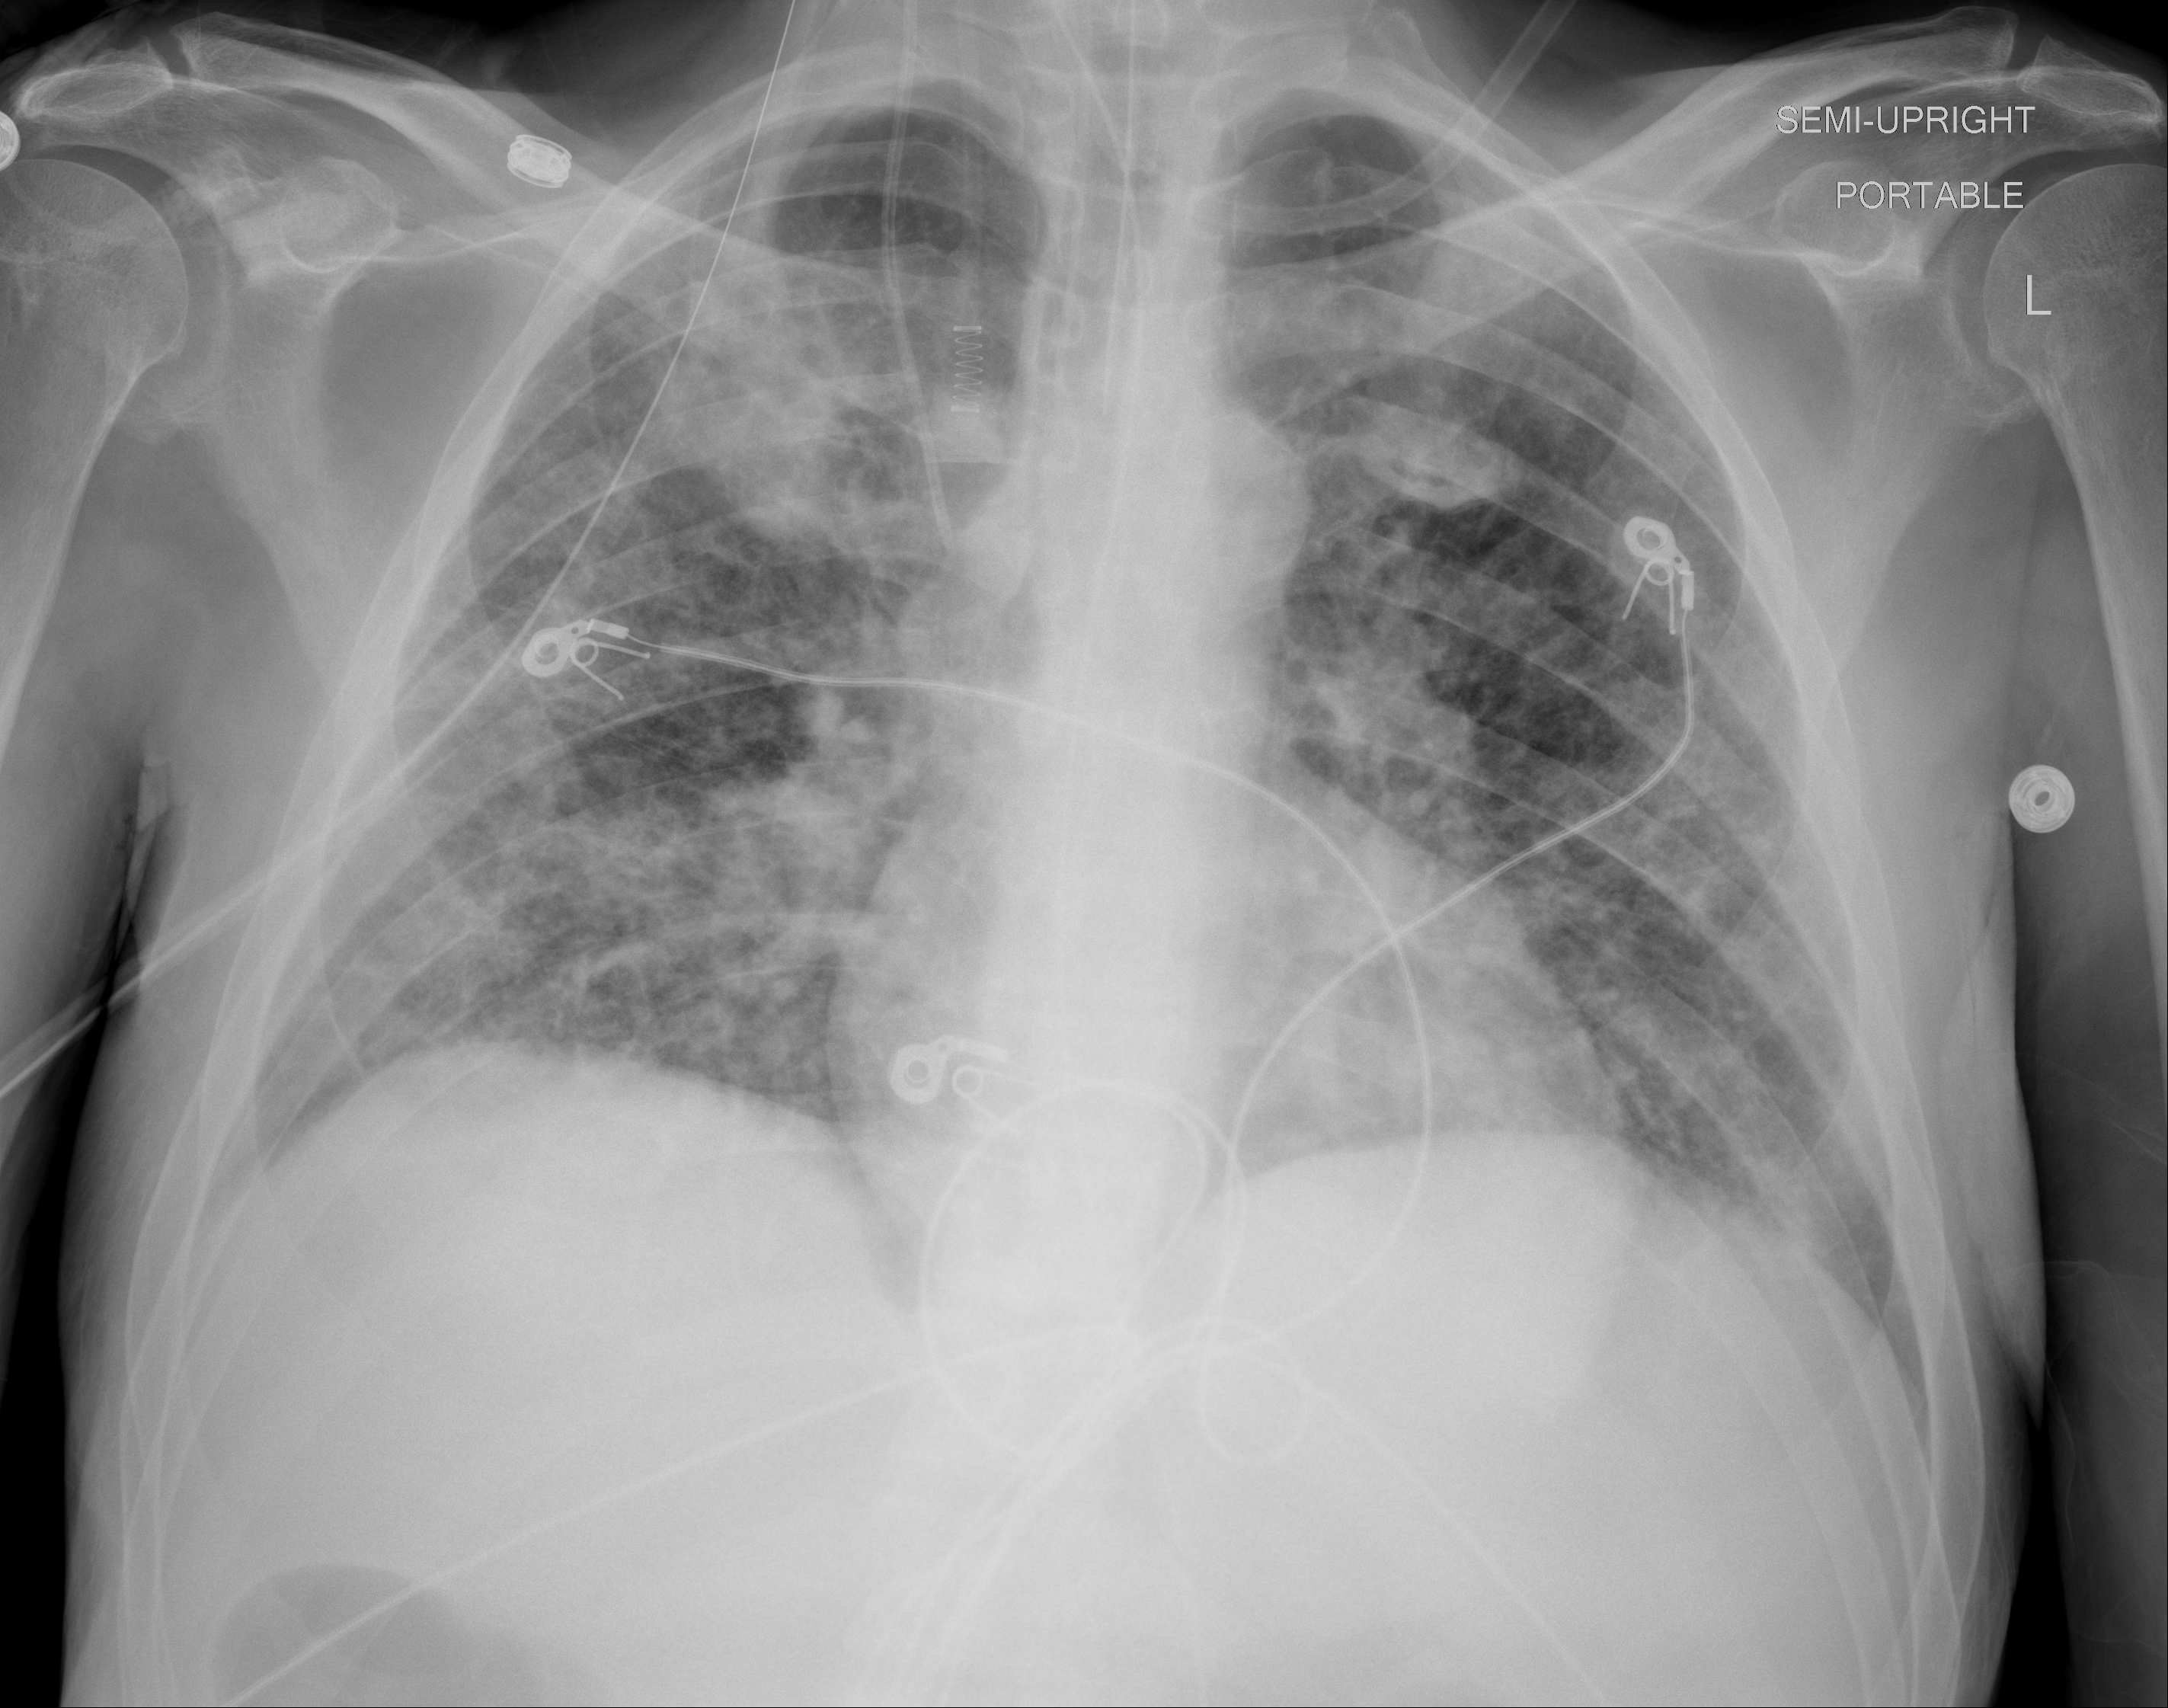
Portable chest radiograph, AP projection. Male patient, age 54 years; imaged 9 days after the COVID-19 diagnosis.
Radiologist's key findings for this exam: Patchy lung opacities again noted bilaterally, possibly increased within the right lung base.